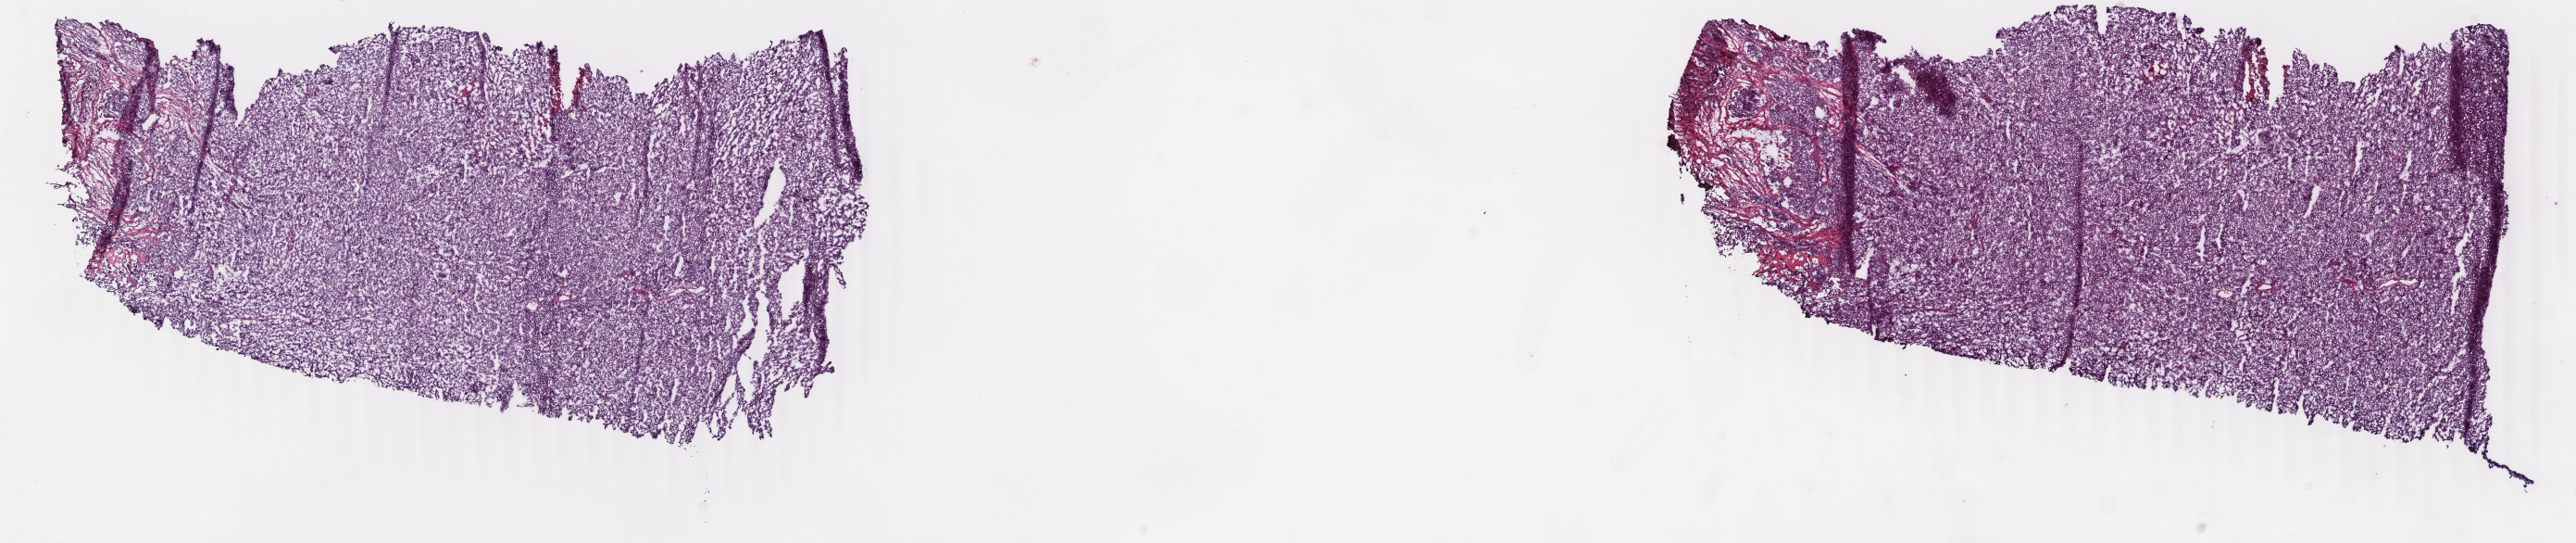
Digitized H&E tissue section (whole slide), low-resolution overview of the scanned area, about 22.1 x 4.7 mm; frozen section from the bottom of the tissue portion; uterus, primary tumour sample. Patient: female, age at initial diagnosis 69 years. Histologic grade: G3 (poorly differentiated). Composition of this section per pathologist review: tumour cells 90%, tumour nuclei 98%, normal cells 0%, stromal cells 6%, necrosis 4%. Inflammatory infiltration, as recorded: lymphocyte infiltration 0%, monocyte infiltration 0%, neutrophil infiltration 0%.
Diagnosis: Endometrioid adenocarcinoma, NOS (endometrium). FIGO stage: IA.